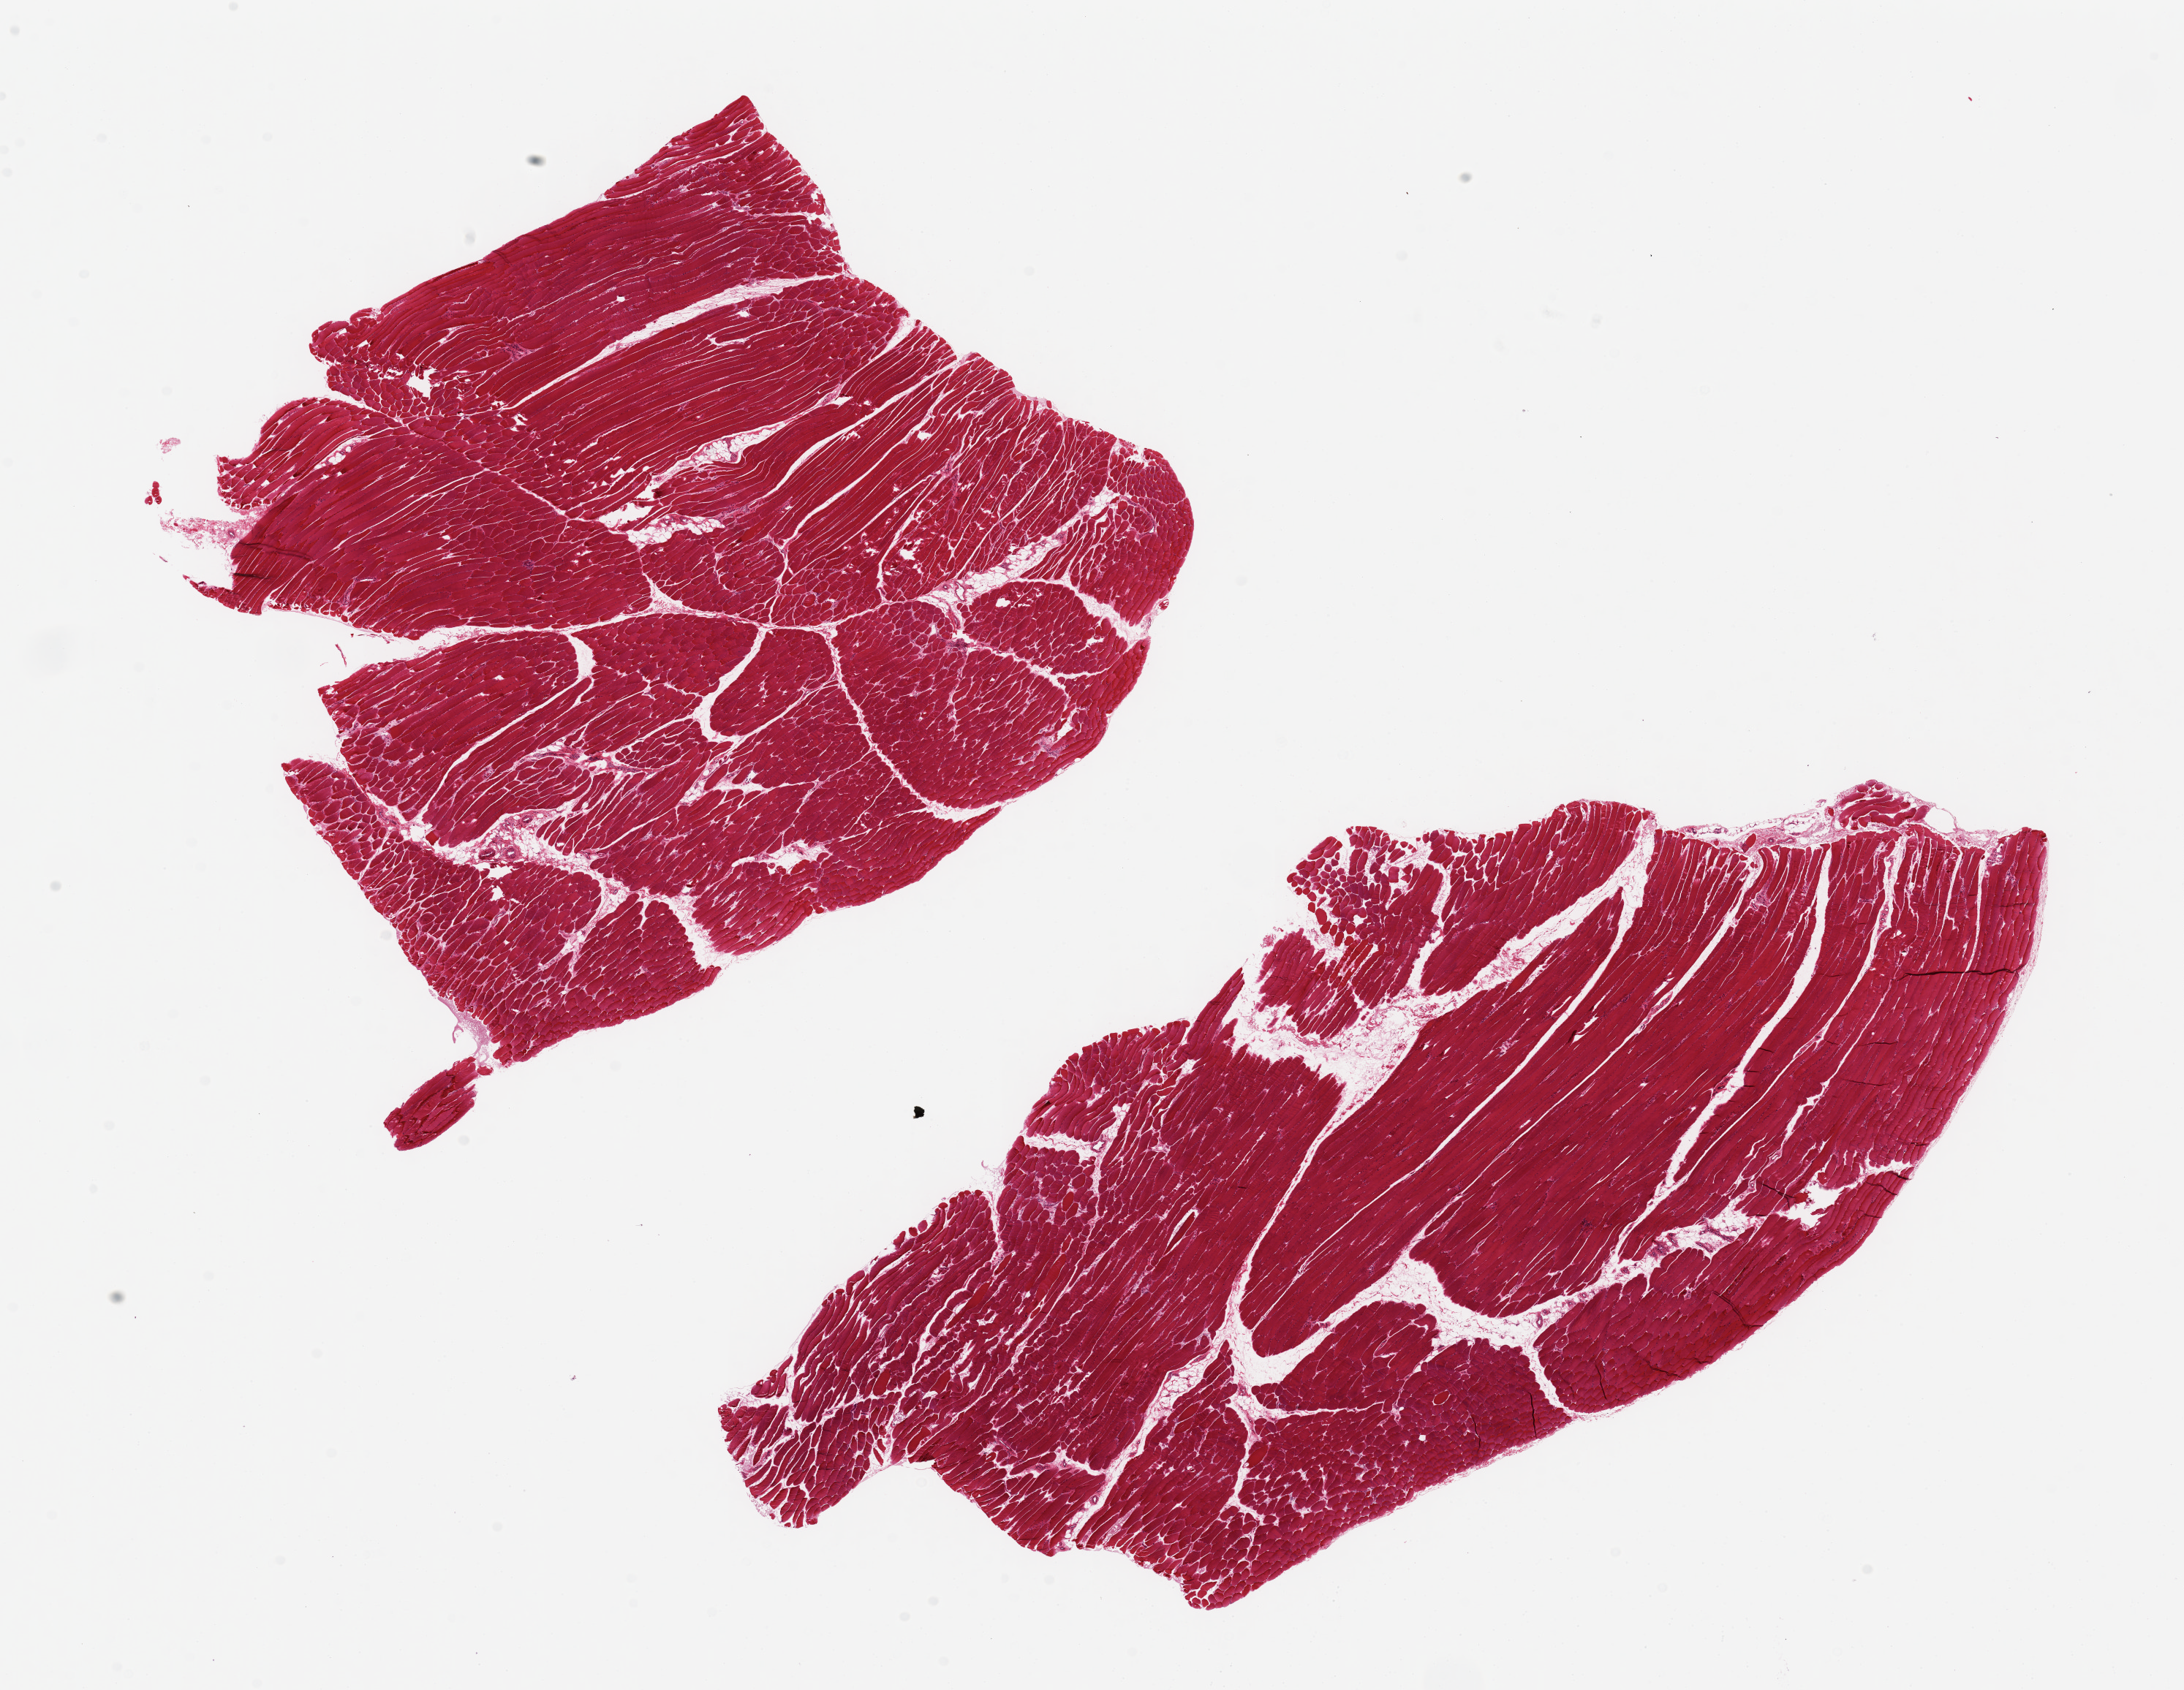
Hematoxylin and eosin (H&E) whole-slide image, a low-resolution overview of the entire scanned area, about 23.6 x 18.3 mm (from a 20x scan), PAXgene-fixed paraffin-embedded (PFPE) section, sampled site (target tissue): skeletal muscle, tissue donor sample. Donor sex: male.
* review note (as recorded): 2 pieces, ~12x7mm. Minimal interstitial fat, excellent specimens